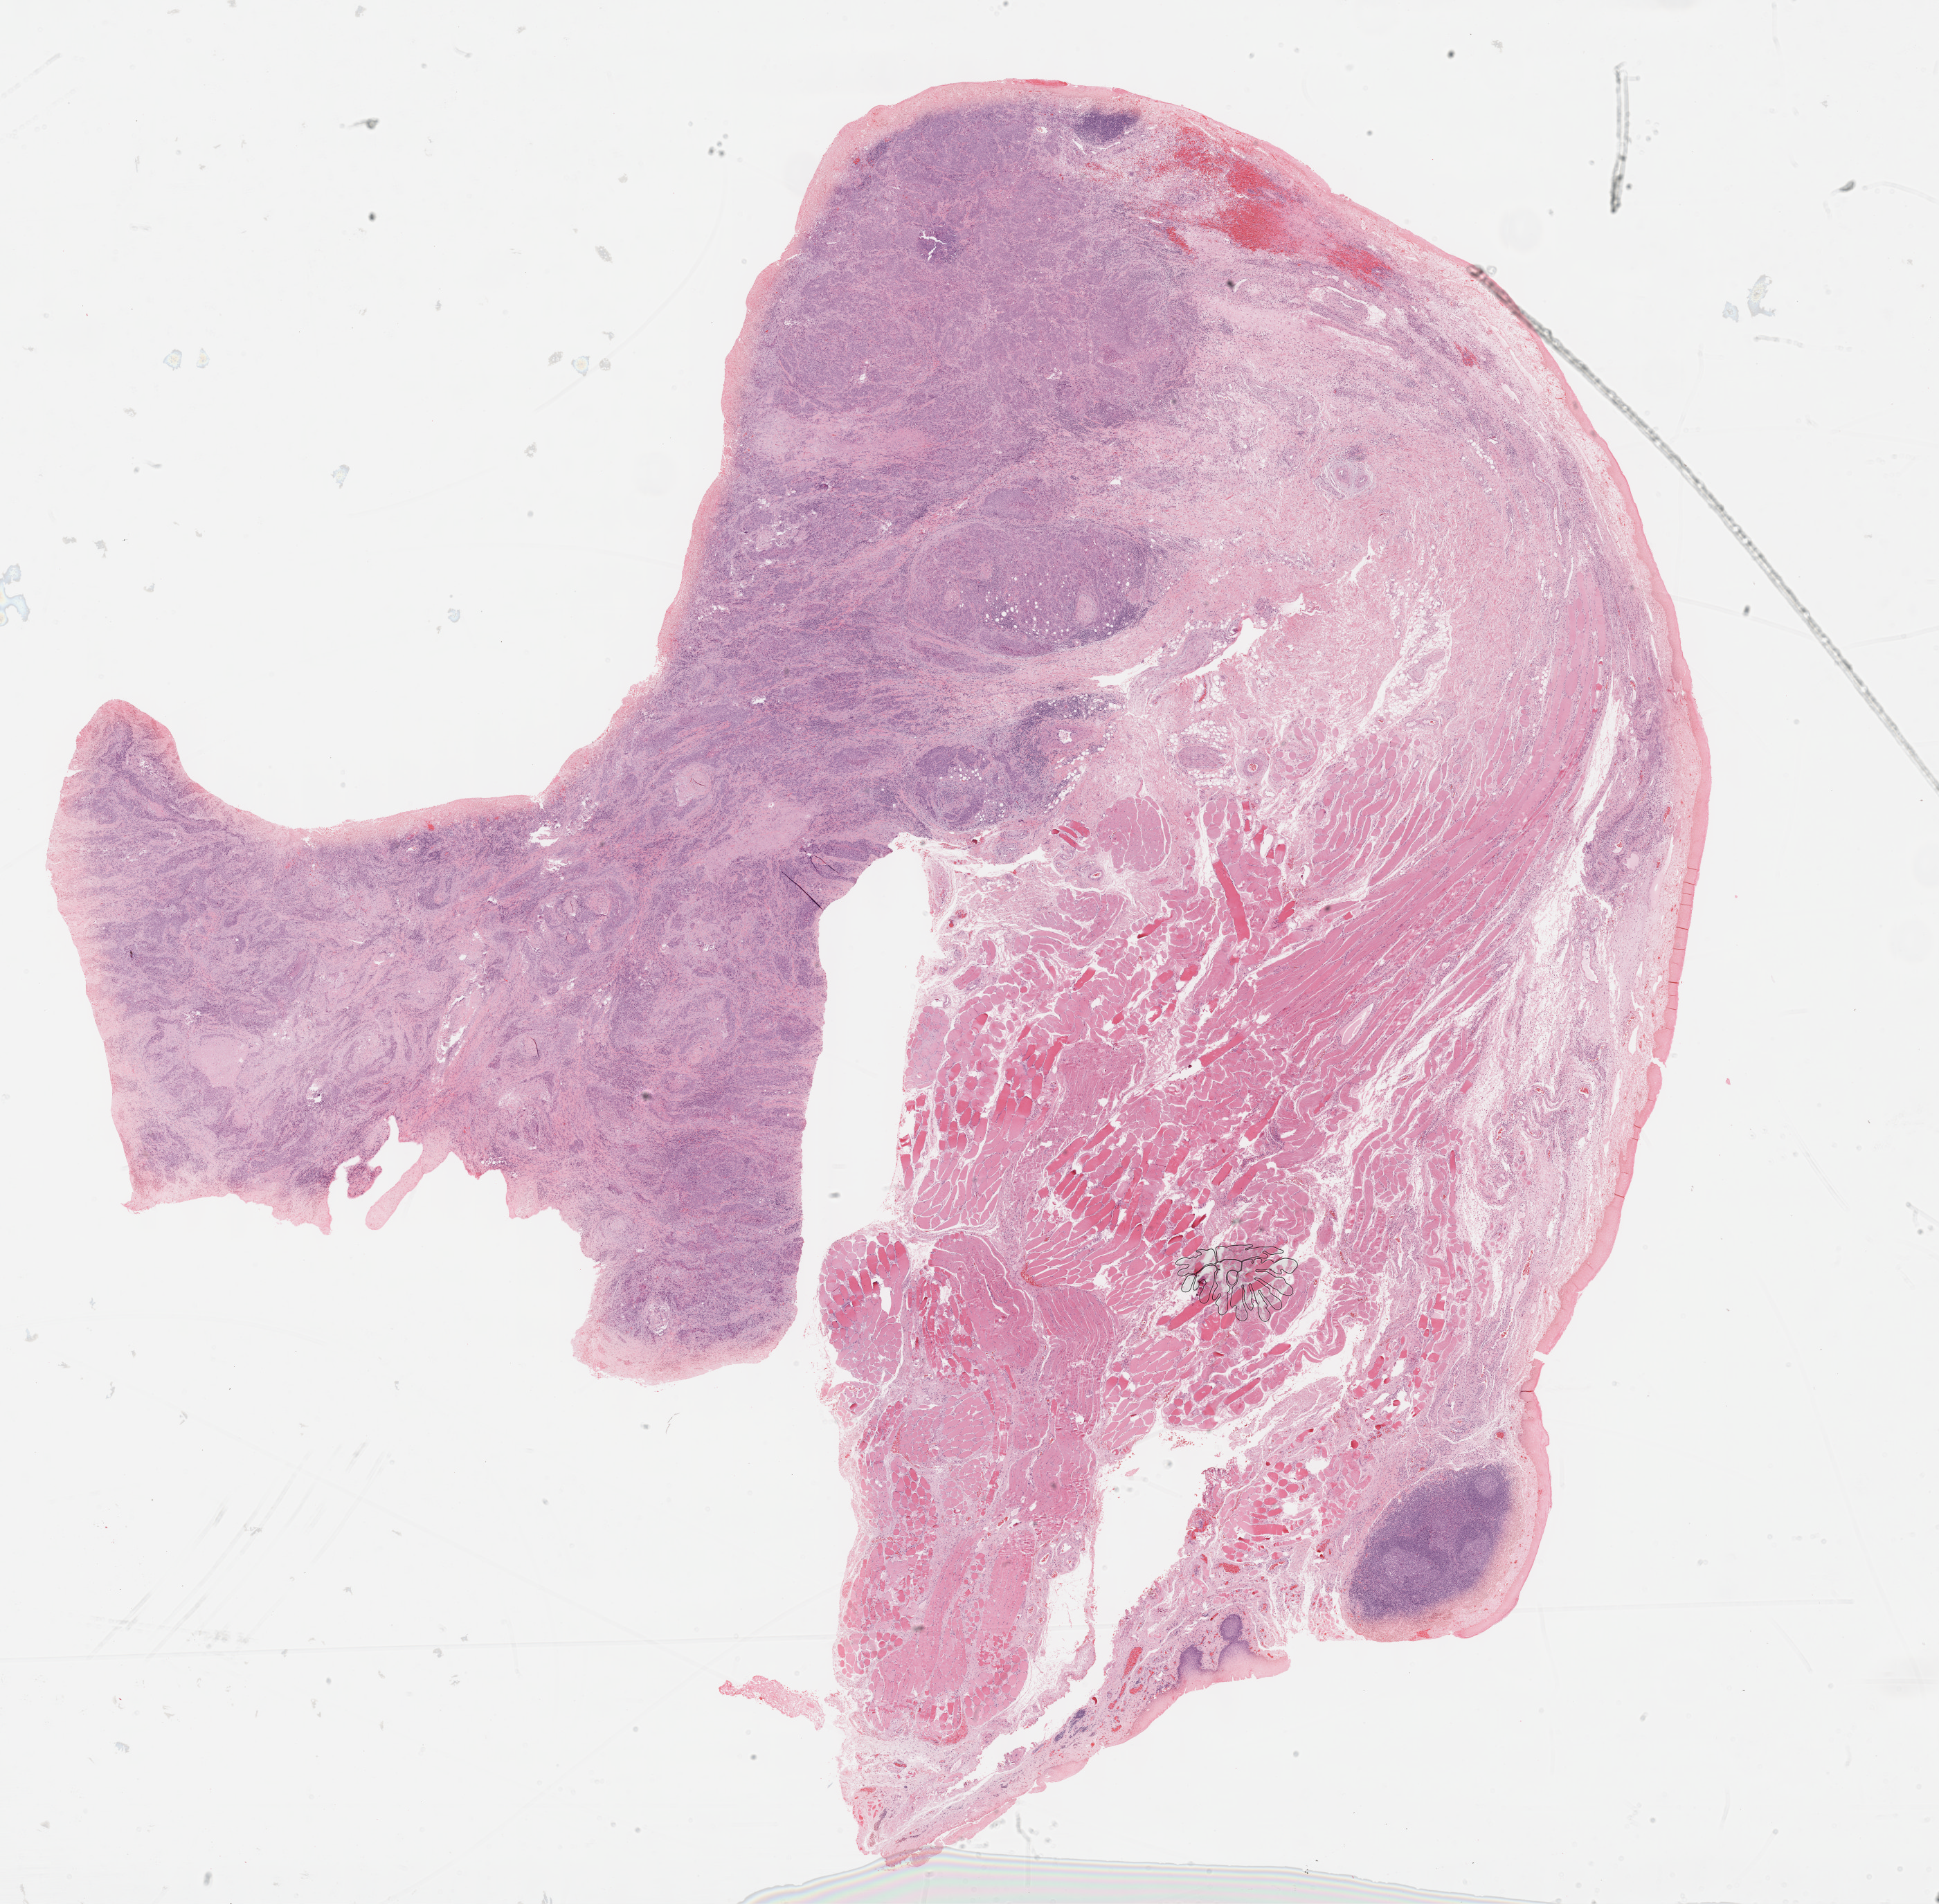
H&E whole-slide image, low-resolution overview of the scanned area, about 22.6 x 22.2 mm. Formalin-fixed paraffin-embedded (FFPE) diagnostic section. Head and neck, primary tumour sample. Male patient; age at initial diagnosis 72 years.
Diagnosis: Squamous cell carcinoma, NOS.